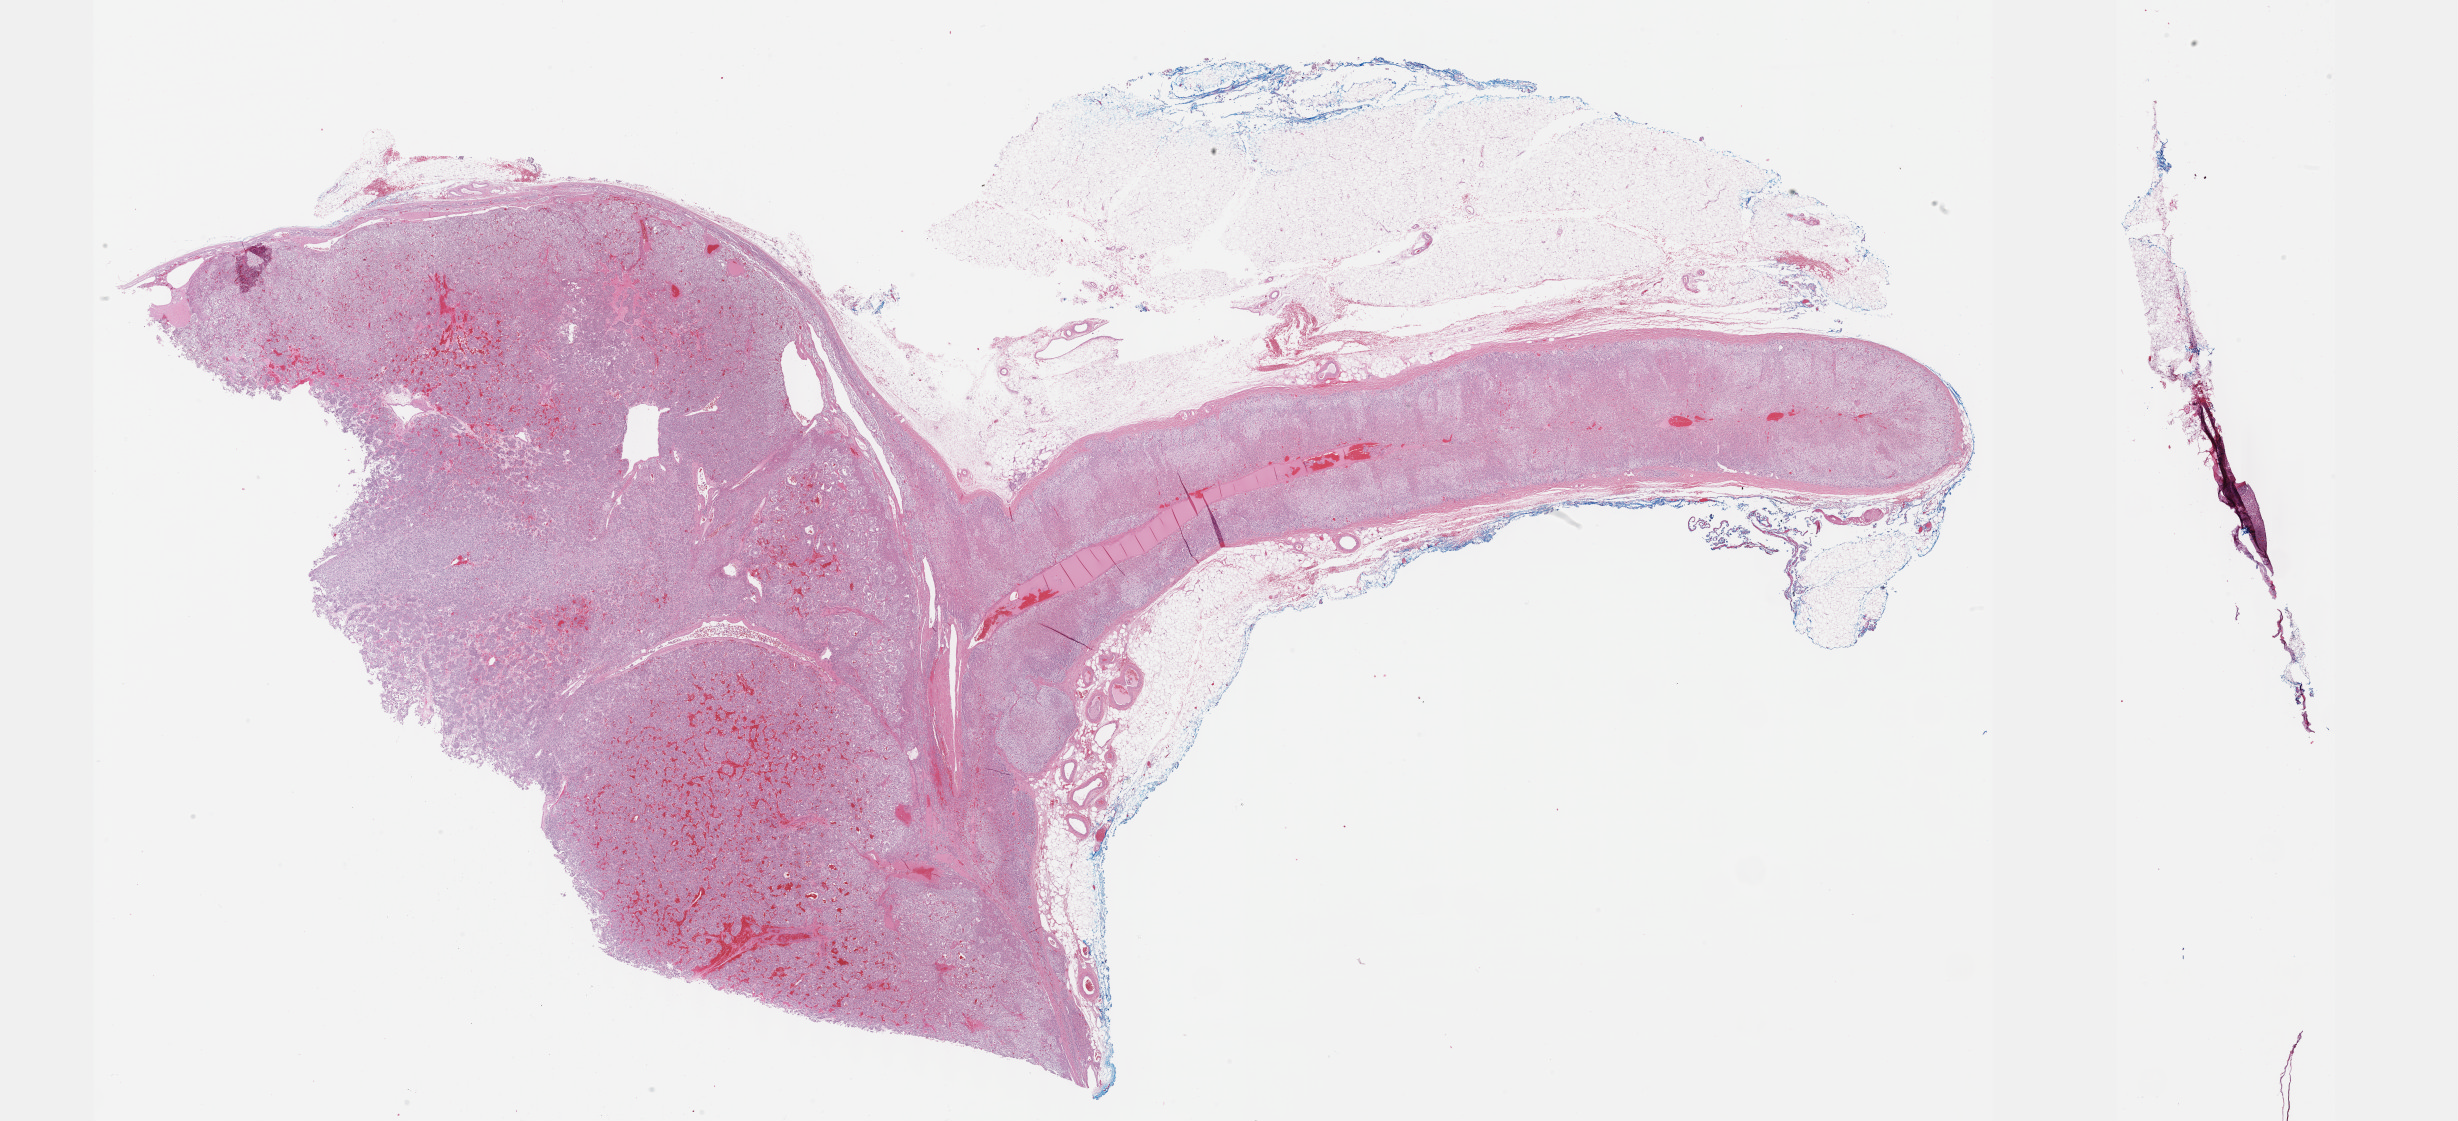
Hematoxylin and eosin (H&E) stained whole-slide image, shown as a low-resolution overview of the whole scanned area (about 39.7 x 18.1 mm, slide scanned at 40x), formalin-fixed paraffin-embedded (FFPE) diagnostic section, adrenal gland, primary tumour sample. Female patient; age at initial diagnosis 51 years.
Pathologic diagnosis: Pheochromocytoma, NOS.